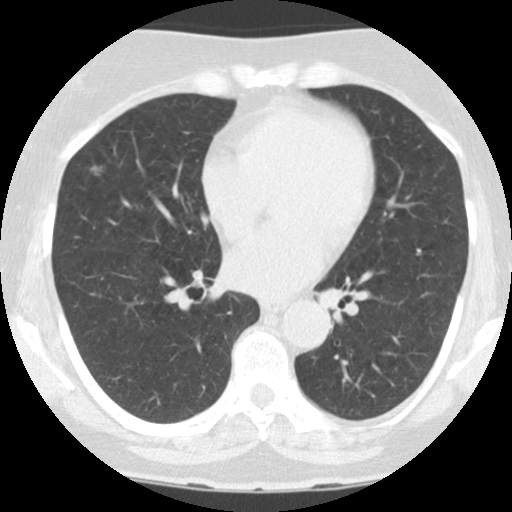
Low-dose screening chest CT, axial slice. Baseline annual screen. Lung window (W 1500 / L -600 HU). 2.5 mm slice thickness. Standard (soft-tissue) reconstruction kernel (STANDARD). 512 × 512 image matrix. Female, age 60 years at enrolment. Former smoker at enrolment.
Lesion marked by an expert reader, bounding box <83,159,111,183> (left, top, right, bottom; pixels). The screening reader recorded 3 non-calcified nodules or masses ≥4 mm on this exam (left upper lobe, right upper lobe, right upper lobe); which of them this box marks is not recorded. Official screen result: positive, change unspecified: nodule(s) >= 4 mm or enlarging nodule(s), mass(es), or other non-specific abnormalities suspicious for lung cancer. Lung cancer was diagnosed 31 days after this screen: bronchiolo-alveolar adenocarcinoma, NOS, left upper lobe, moderately differentiated (G2), stage IA (AJCC 6th edition), 15 mm at pathology.